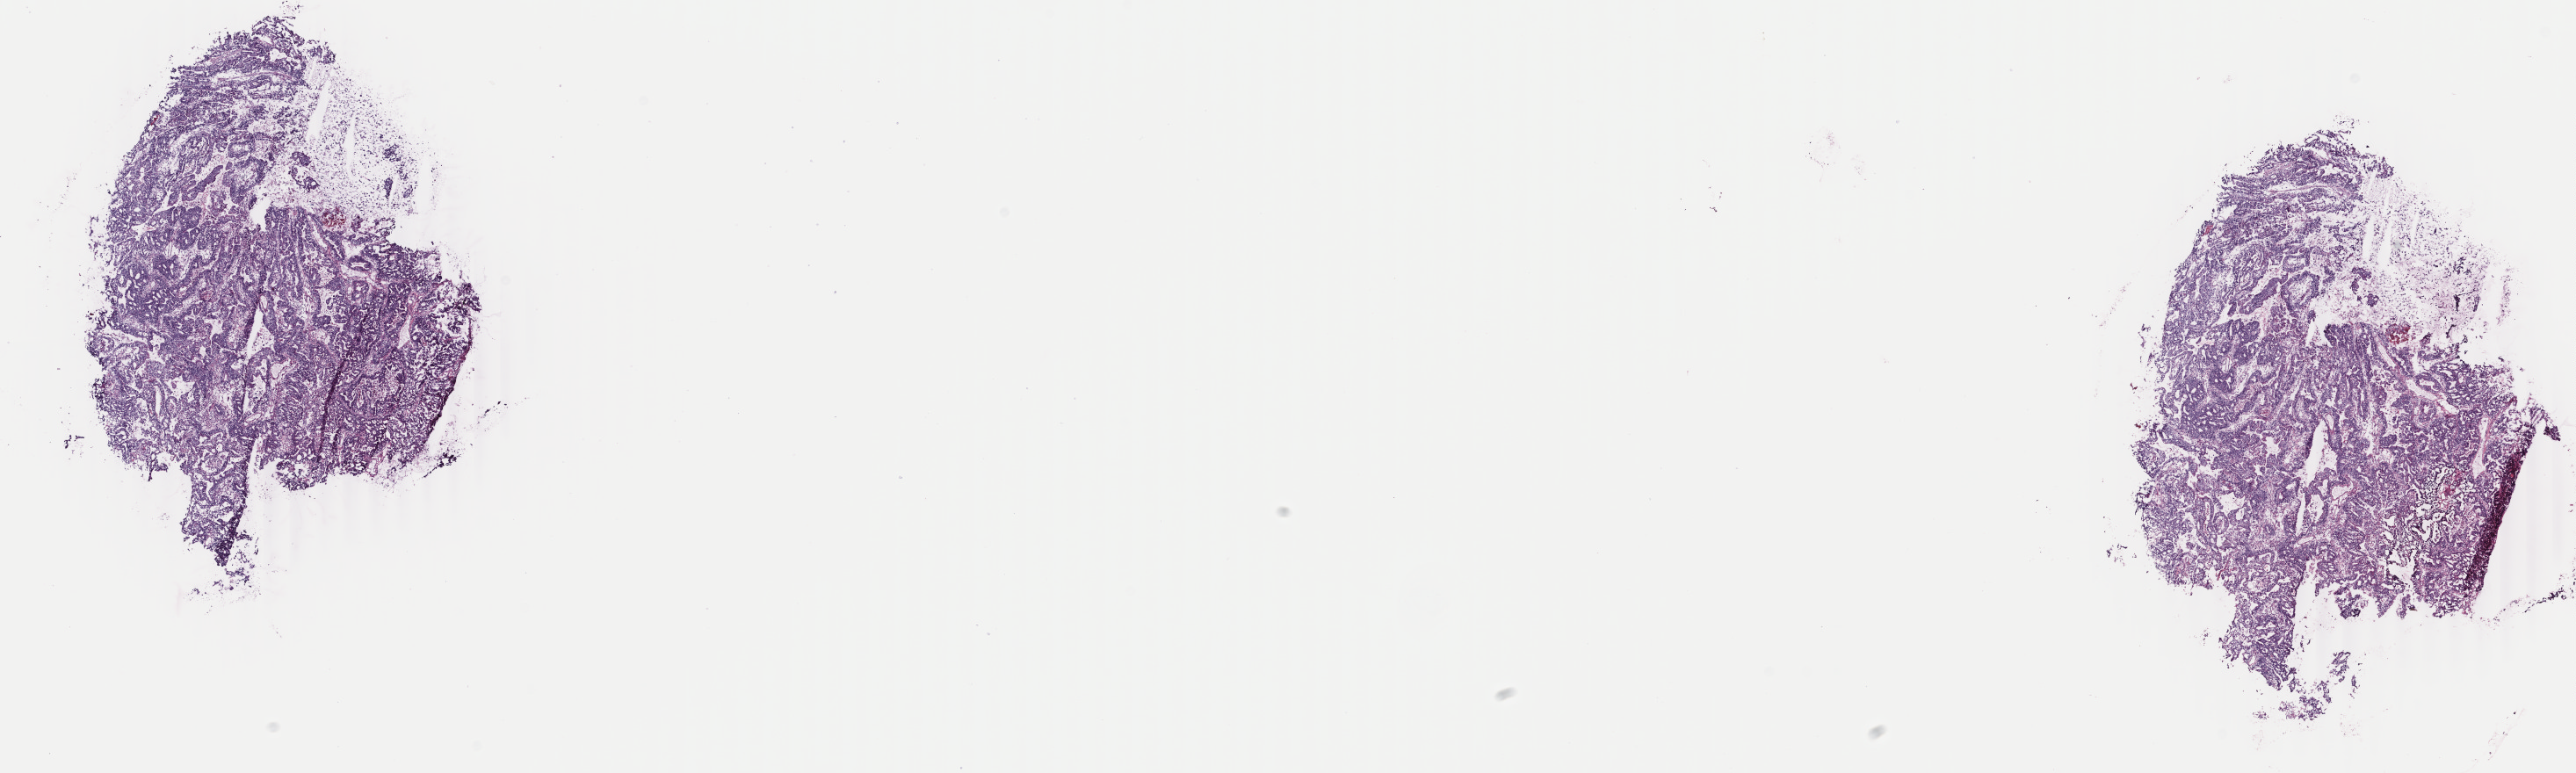
Digitized H&E-stained tissue section (whole slide), a low-resolution overview of the entire scanned area, about 23.3 x 7.0 mm (acquisition: 40x scan); frozen section from the top of the tissue portion; primary tumour sample from the esophagus. Male, age 62 years at initial diagnosis. Histologic grade: G2 (moderately differentiated). Slide review estimates, as recorded: tumour cells 93%, tumour nuclei 75%, normal cells 0%, stromal cells 0%, necrosis 7%. Infiltration values recorded for this section: lymphocyte infiltration 0%, monocyte infiltration 0%, neutrophil infiltration 0%.
Lymph nodes positive (case pathology): 15 of 20 examined. AJCC pathologic stage: IIIC (7th edition). Diagnosis: Adenocarcinoma, NOS.